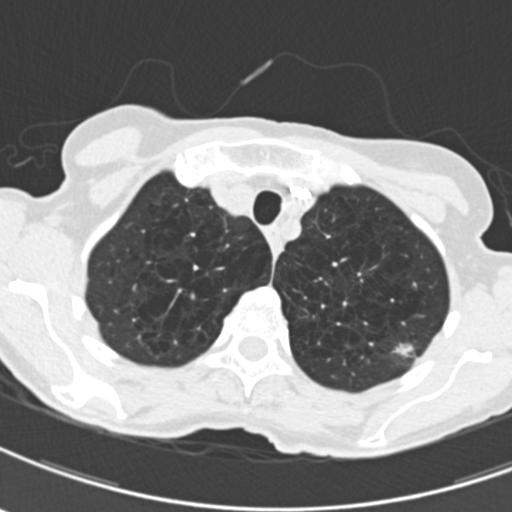
Chest CT (low-dose screening protocol), one axial image. Third screening round (two years after baseline). Lung window (W 1500 / L -600 HU). Standard (soft-tissue) reconstruction kernel (B30f). Slice 37 of 203 in the series. 512 × 512 image matrix. Female participant, aged 71 years at enrolment.
Expert reader's lesion annotation, bounding box <385,332,426,371> (left, top, right, bottom; pixels). Screening reader's record for this exam (one nodule recorded; not confirmed to be the boxed lesion): non-calcified nodule or mass ≥4 mm, left upper lobe, 12 × 9 mm, spiculated (stellate) margins, mixed attenuation, pre-existing on the prior screen: yes; interval growth: yes. Official screen result: positive, other. Lung cancer was diagnosed 114 days after this screen: adenocarcinoma, NOS, left upper lobe, moderately differentiated (G2), stage IA (AJCC 6th edition), 12 mm at pathology.